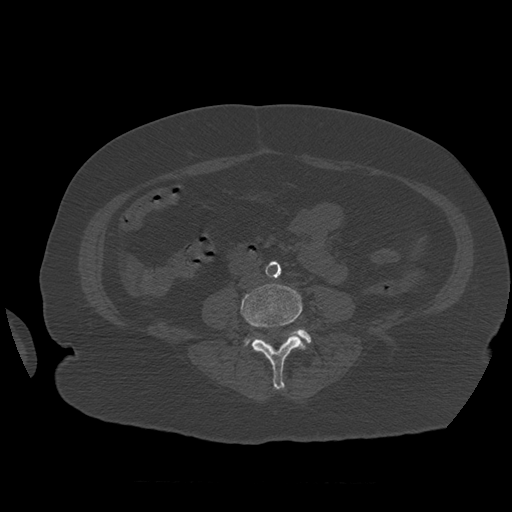
CT including the spine, one axial slice; position 200 of 399 along the scan axis; reconstruction kernel STANDARD; bone window (W 1800 / L 400 HU); 512 × 512 image matrix, field of view 404 × 404 mm. Patient age 81 years. Case-level facts recorded for this patient, not image findings: primary cancer: renal.
Annotated regions visible in this slice (semi-automatically segmented with operator editing):
- L4 vertebra: bounding box <241,284,306,390> (left, top, right, bottom; pixels)
- L5 vertebra: <245,329,312,345>